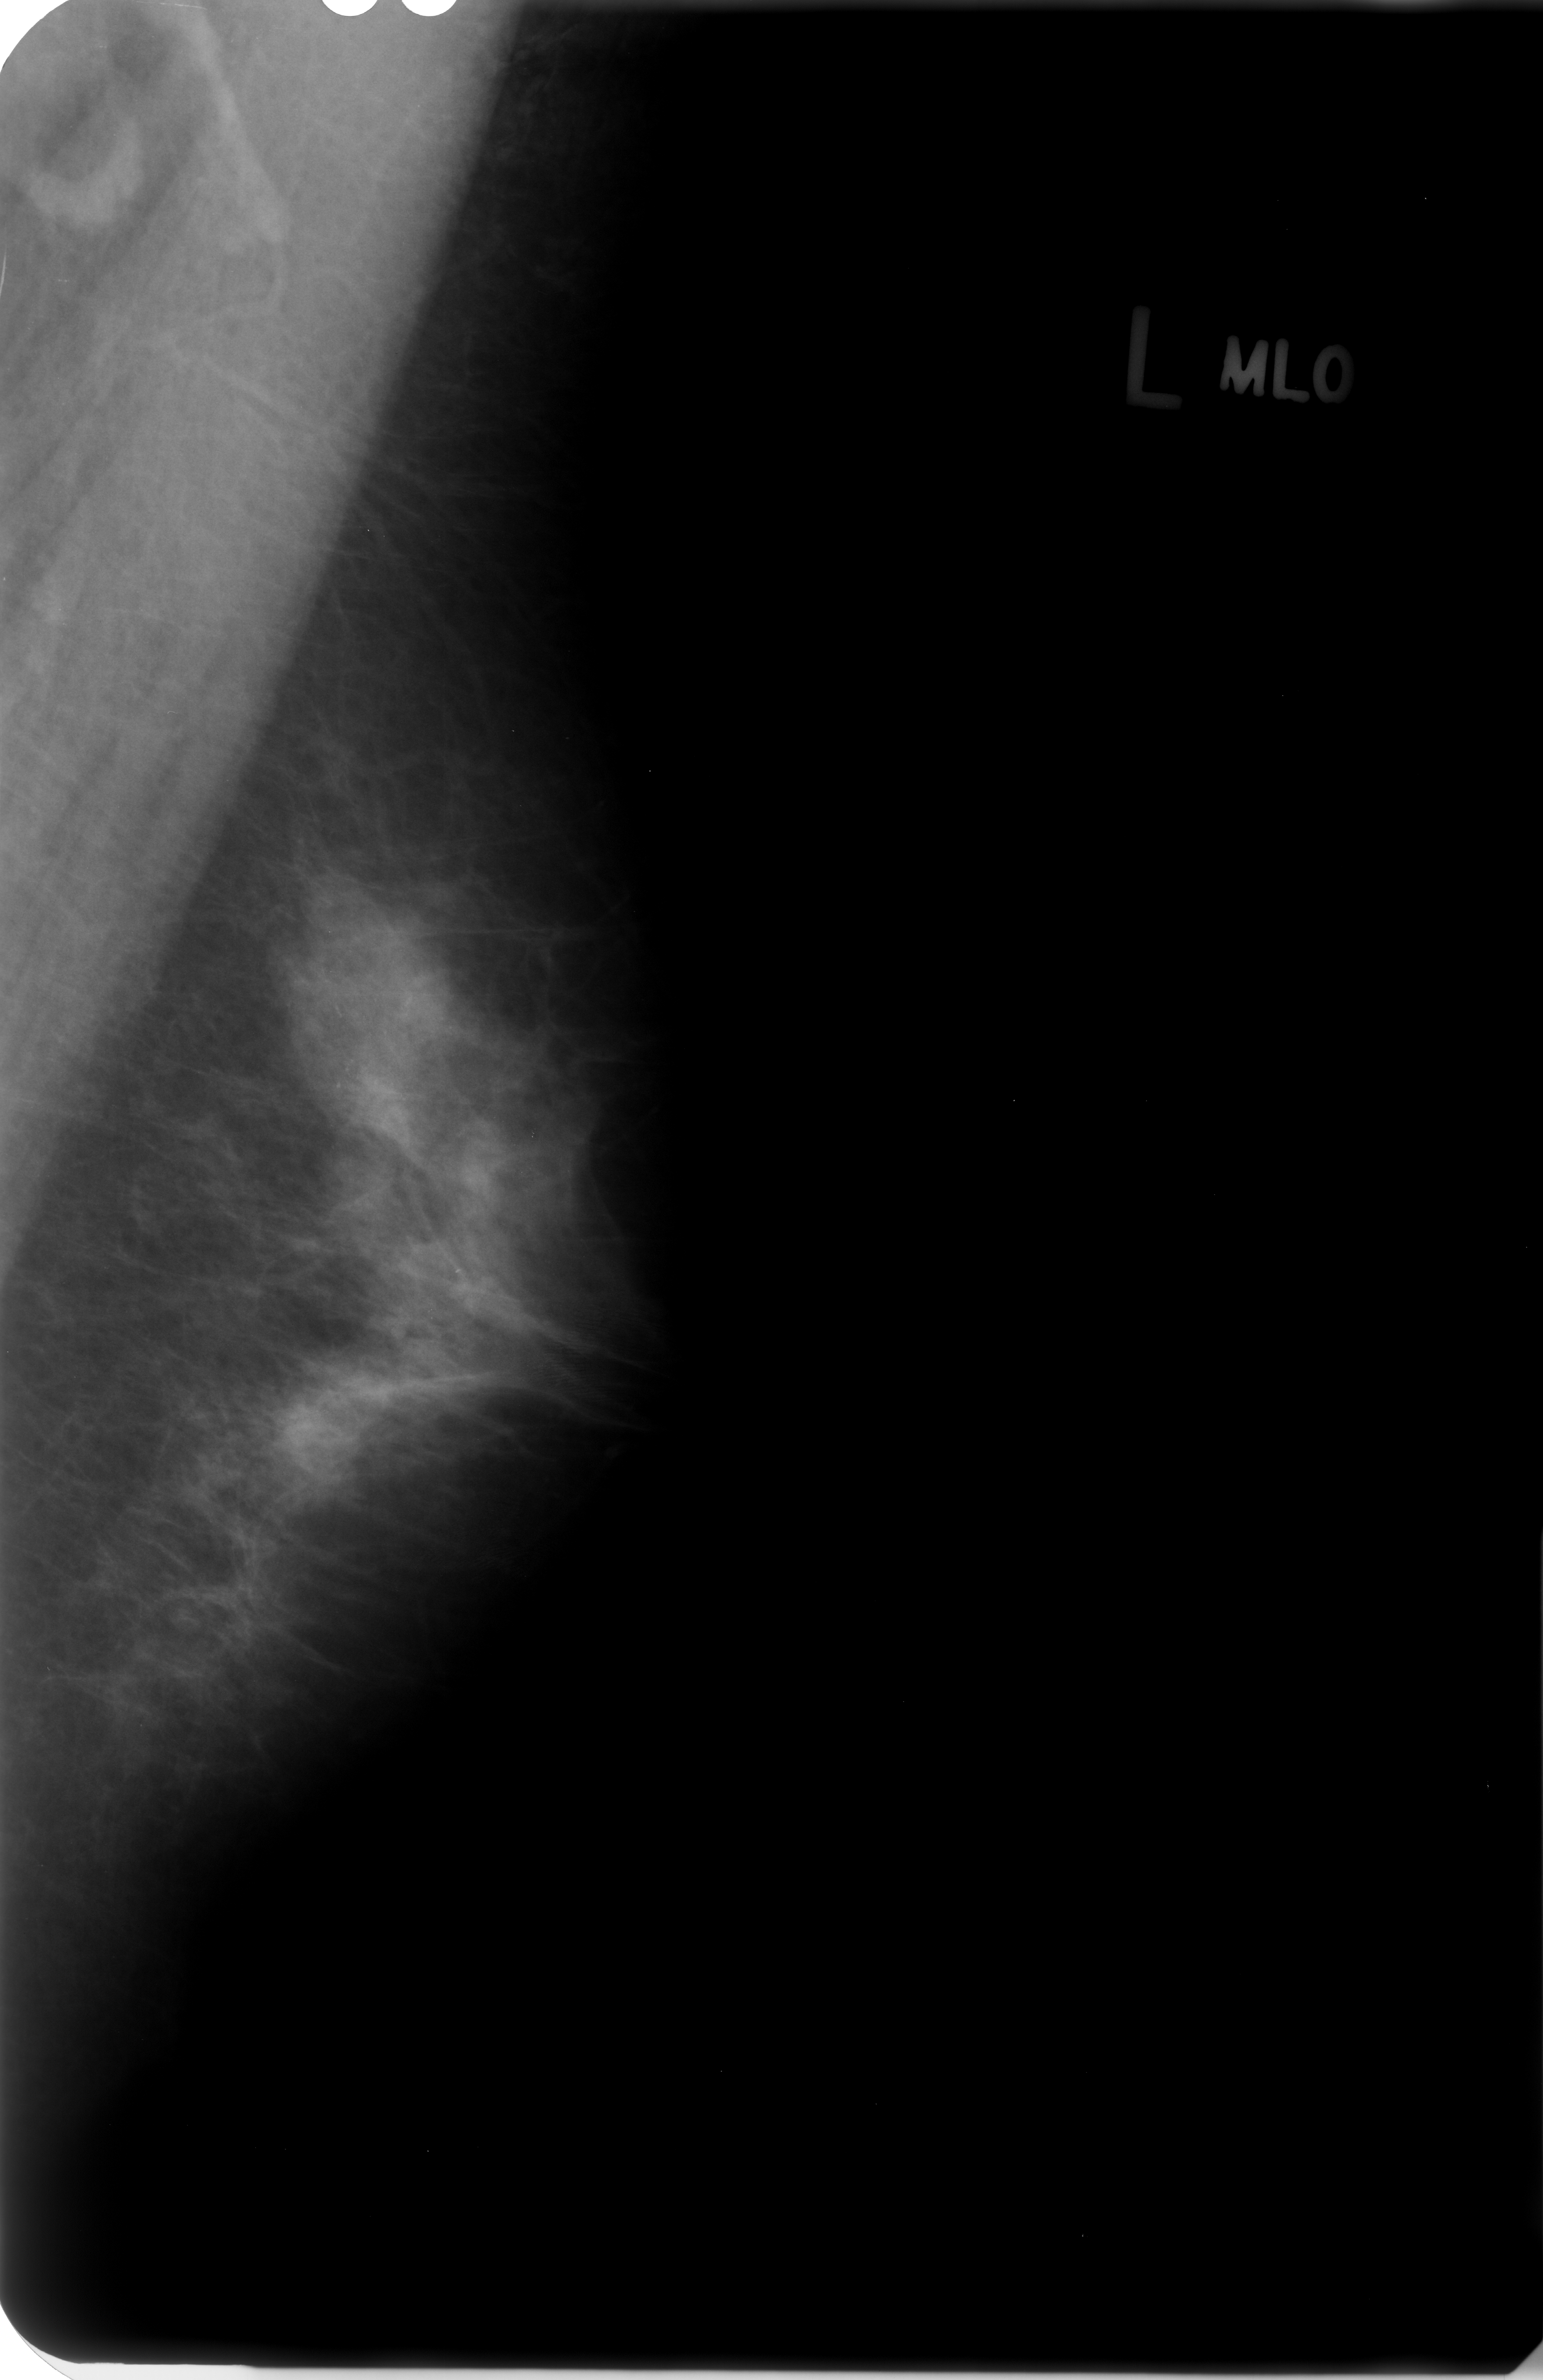
Digitized screen-film mammogram, left breast, mediolateral oblique (MLO) view, BI-RADS breast density category 2 (scale 1–4).
Radiologist-marked abnormalities on this image: calcifications, morphology punctate, distribution segmental; BI-RADS assessment category 4; pathology result (as recorded, not read from the image): benign.